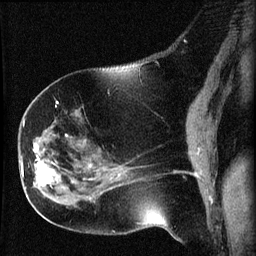
Breast MRI (dynamic contrast-enhanced), one sagittal slice; slice 26 of 60 in the series (ordered by position); dynamic contrast-enhanced series, image 2 of 3 at this slice position (ordered by acquisition); 1.5 T; TE 4.2 ms, TR 8.2 ms; 256 × 256 image matrix, field of view 180 × 180 mm. Patient: female, 63 years.
Annotated regions visible in this slice (semi-automatic segmentation, software-assisted and operator-edited):
- analysis volume of interest (the breast-tissue region the enhancement analysis was run in; not a lesion): bounding box (x1, y1, x2, y2) in pixels: (22, 156, 64, 202)
- tumour enhancement mask (voxels above the 70 % enhancement threshold inside the analysis volume of interest): (22, 156, 53, 187)